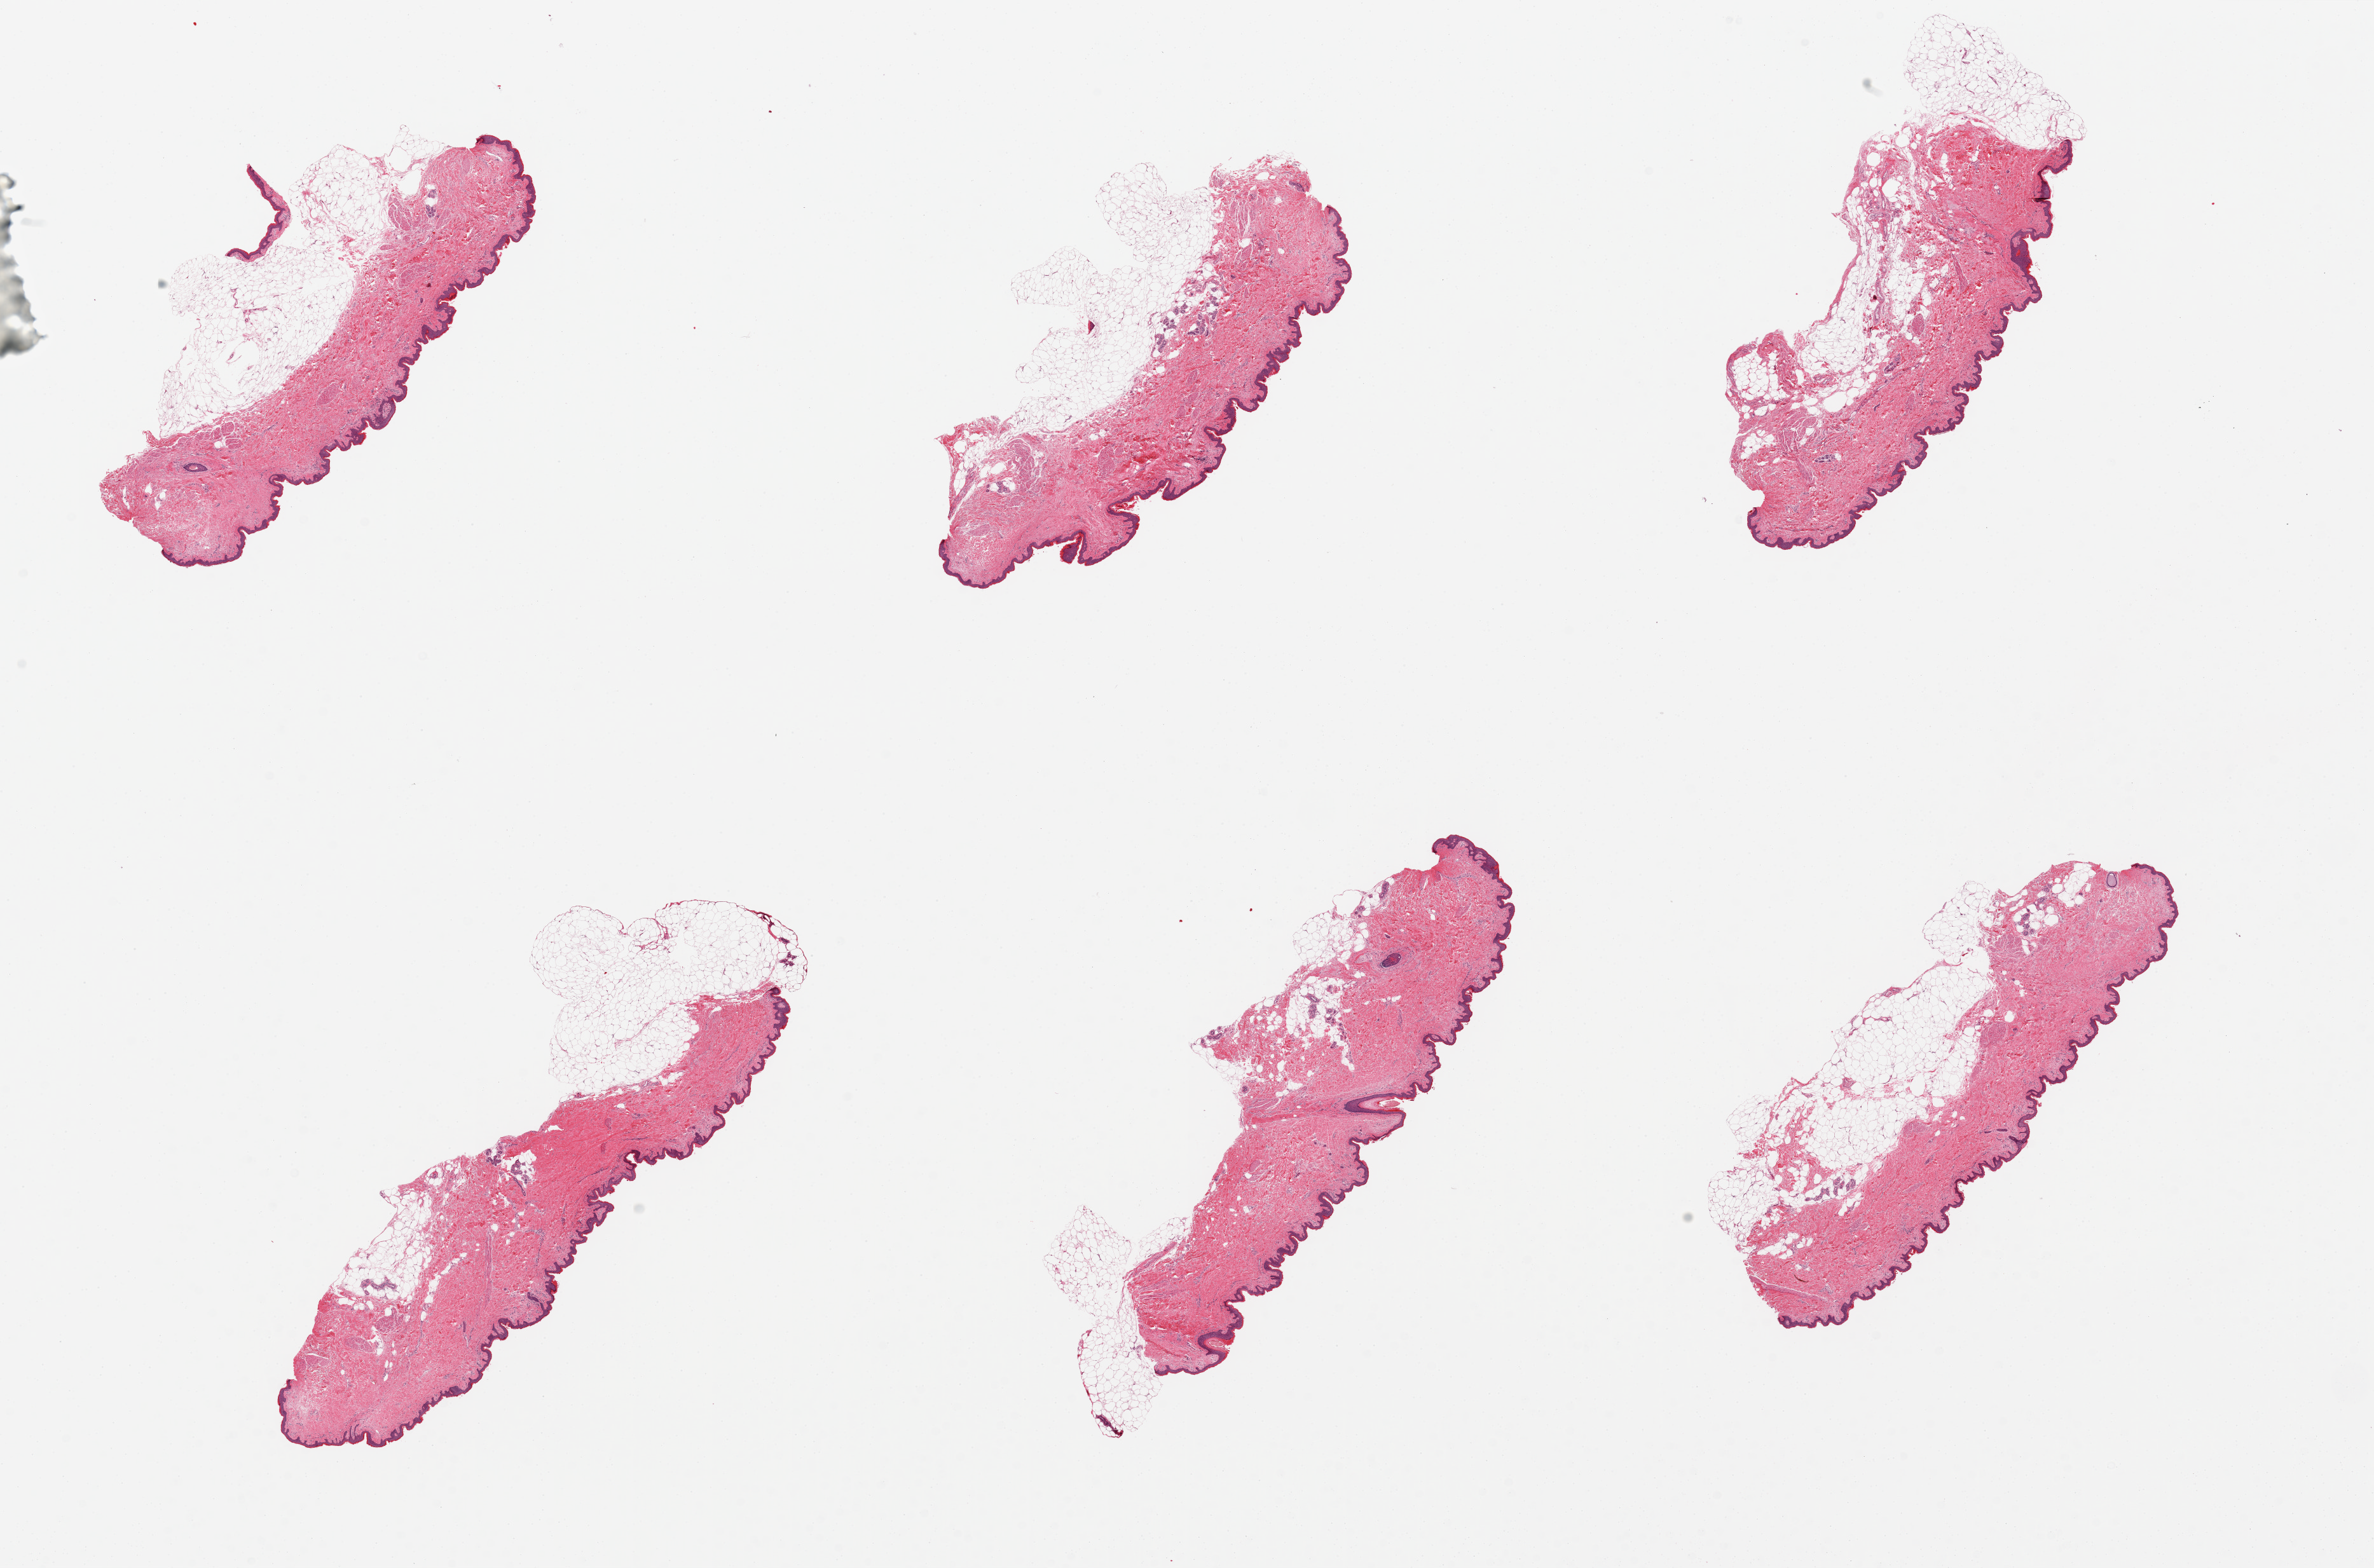
Hematoxylin and eosin (H&E) whole-slide image, whole scanned area (about 29.5 x 19.5 mm) shown as a low-resolution overview. PAXgene-fixed, paraffin-embedded tissue. Target tissue: skin of suprapubic region. Donor tissue sample. Female donor.
Review note (as recorded): 6 pieces, adherent fat on most; squamous epithelium is ~50 microns.